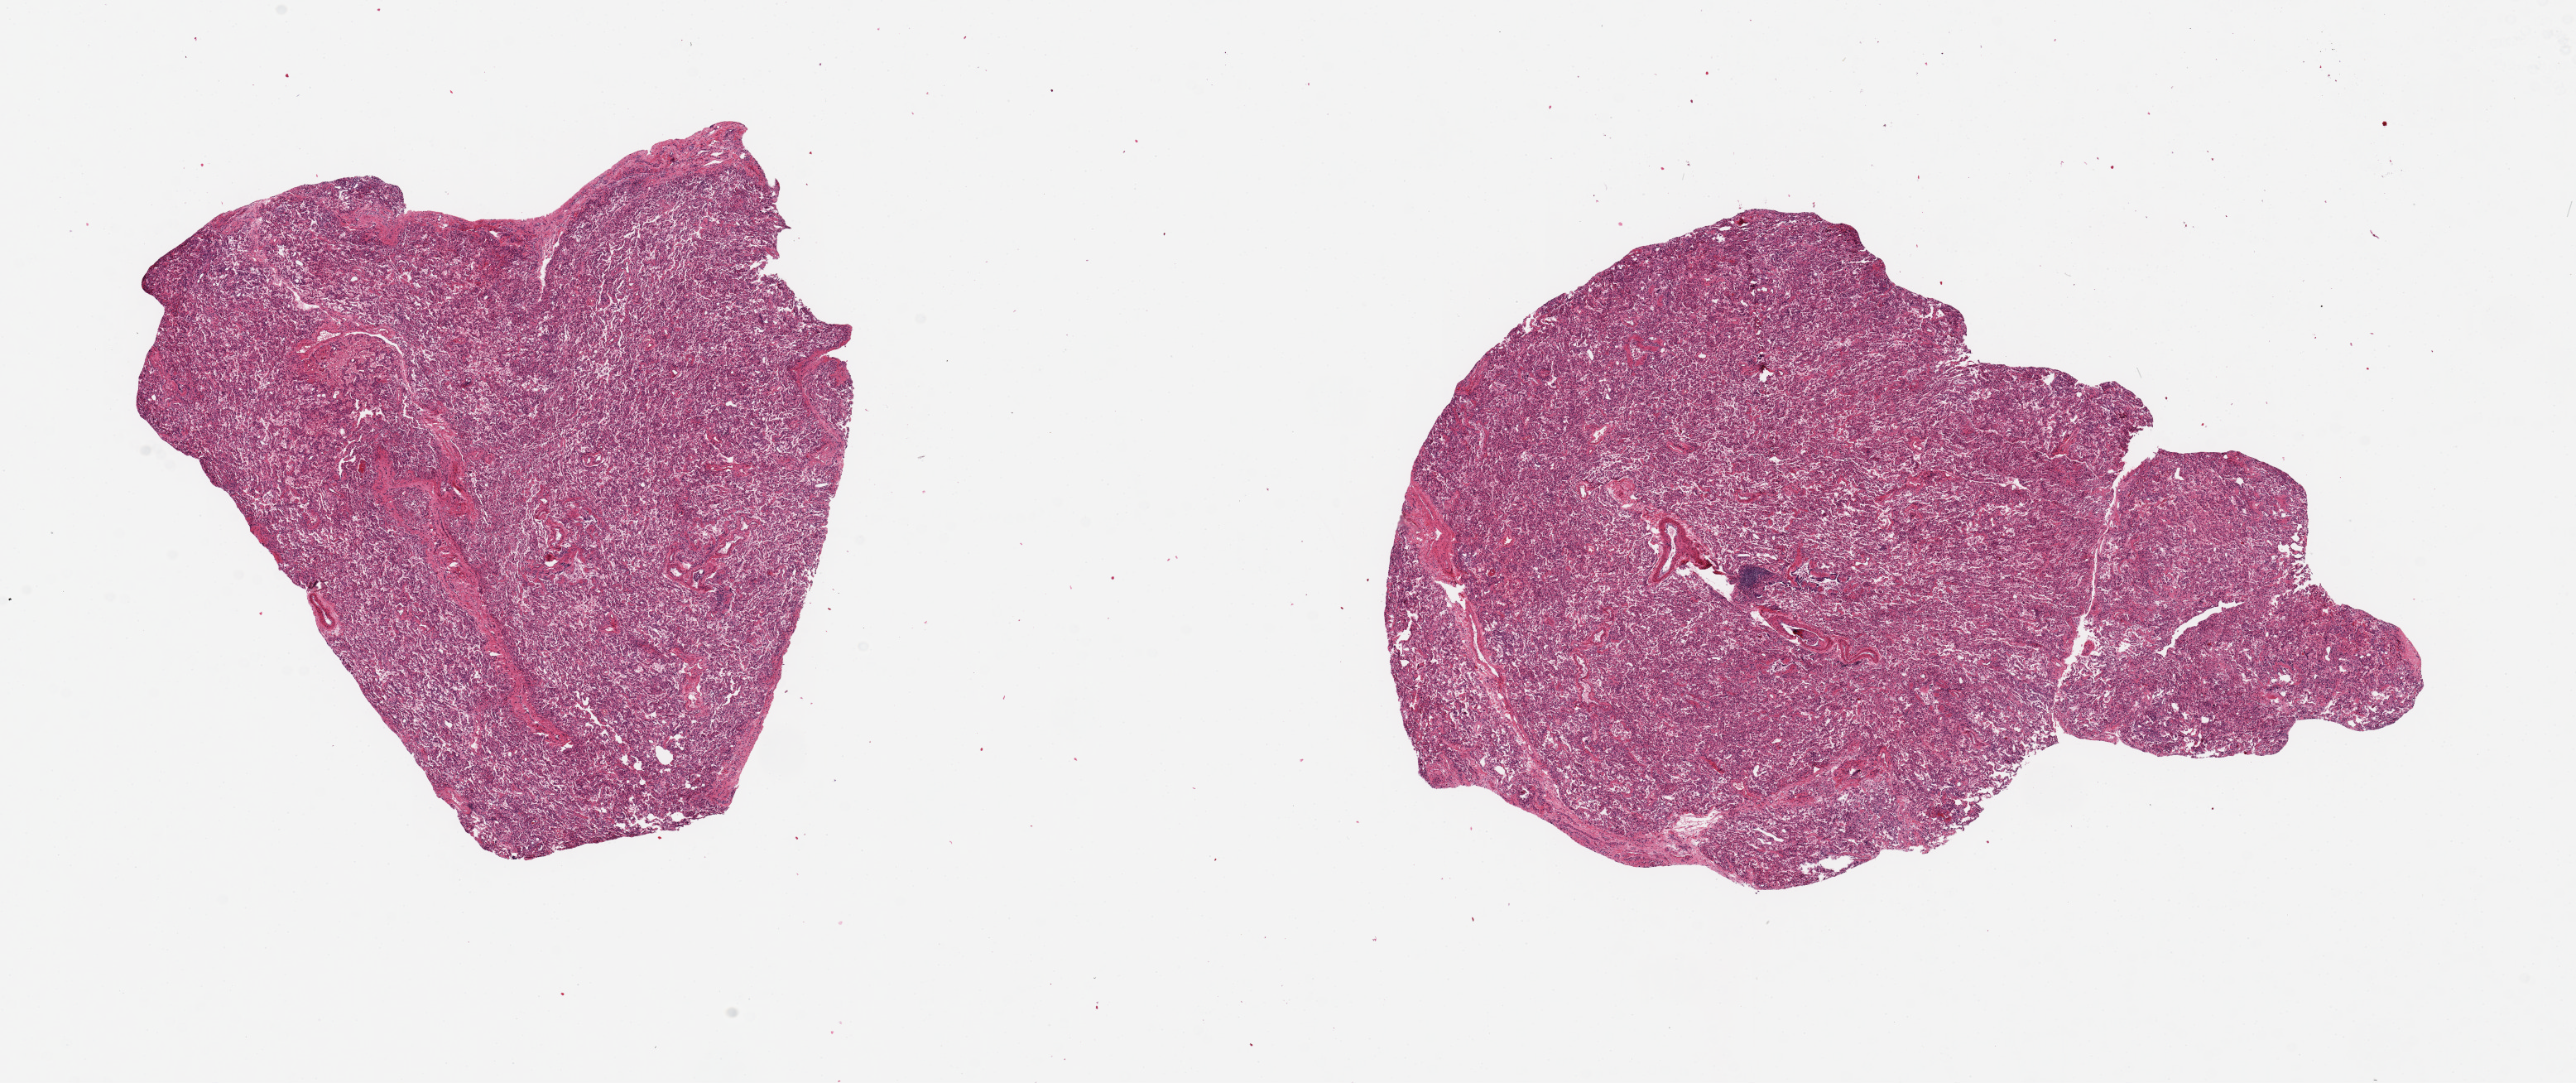
Digitized haematoxylin and eosin-stained section — whole scanned area (about 24.6 x 10.3 mm) shown as a low-resolution overview; PAXgene-fixed paraffin-embedded (PFPE) section; target tissue: lung; tissue donor sample. Donor: female.
* pathologist's review note for this sample: 2 pieces, 10x6.5 & 7x6mm; patchy interstitial fibrosis and pneumonitis